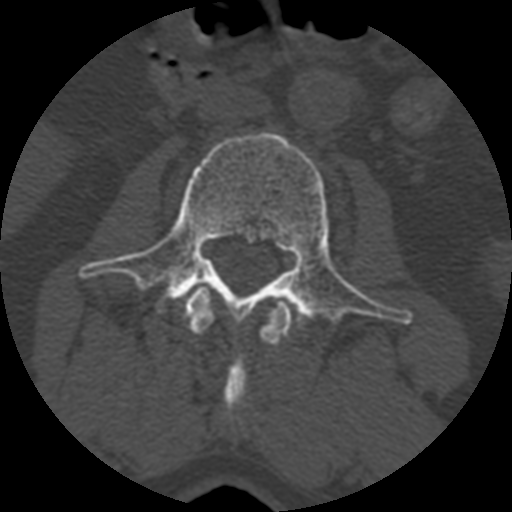
CT including the spine, one axial slice; position 311 of 399 along the scan axis; reconstruction kernel STANDARD; 120 kVp; bone window (W 1800 / L 400 HU); 1.25 mm slice thickness; 512 × 512 image matrix, field of view 160 × 160 mm. Patient age 71 years. Case-level facts recorded for this patient, not image findings: primary cancer: prostate.
Annotated regions visible in this slice (semi-automatic segmentation, software-assisted and operator-edited):
- L2 vertebra: box from (x=181, y=287) to (x=292, y=411) px
- L3 vertebra: (x=79, y=132)–(x=406, y=327)